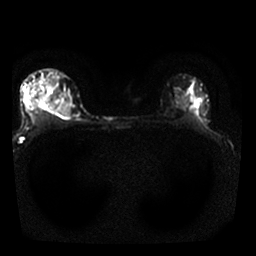
Breast MRI, one axial slice; position 19 of 25 along the scan axis; diffusion-weighted series; image 2 of 4 stored at this slice position (different b-values; order by instance number); 1.5 T; 4 mm slice thickness; 256 × 256 image matrix. Female patient.
Outlined on this slice (expert manual segmentation):
- tumour on diffusion-weighted imaging: box from (x=40, y=98) to (x=69, y=116) px